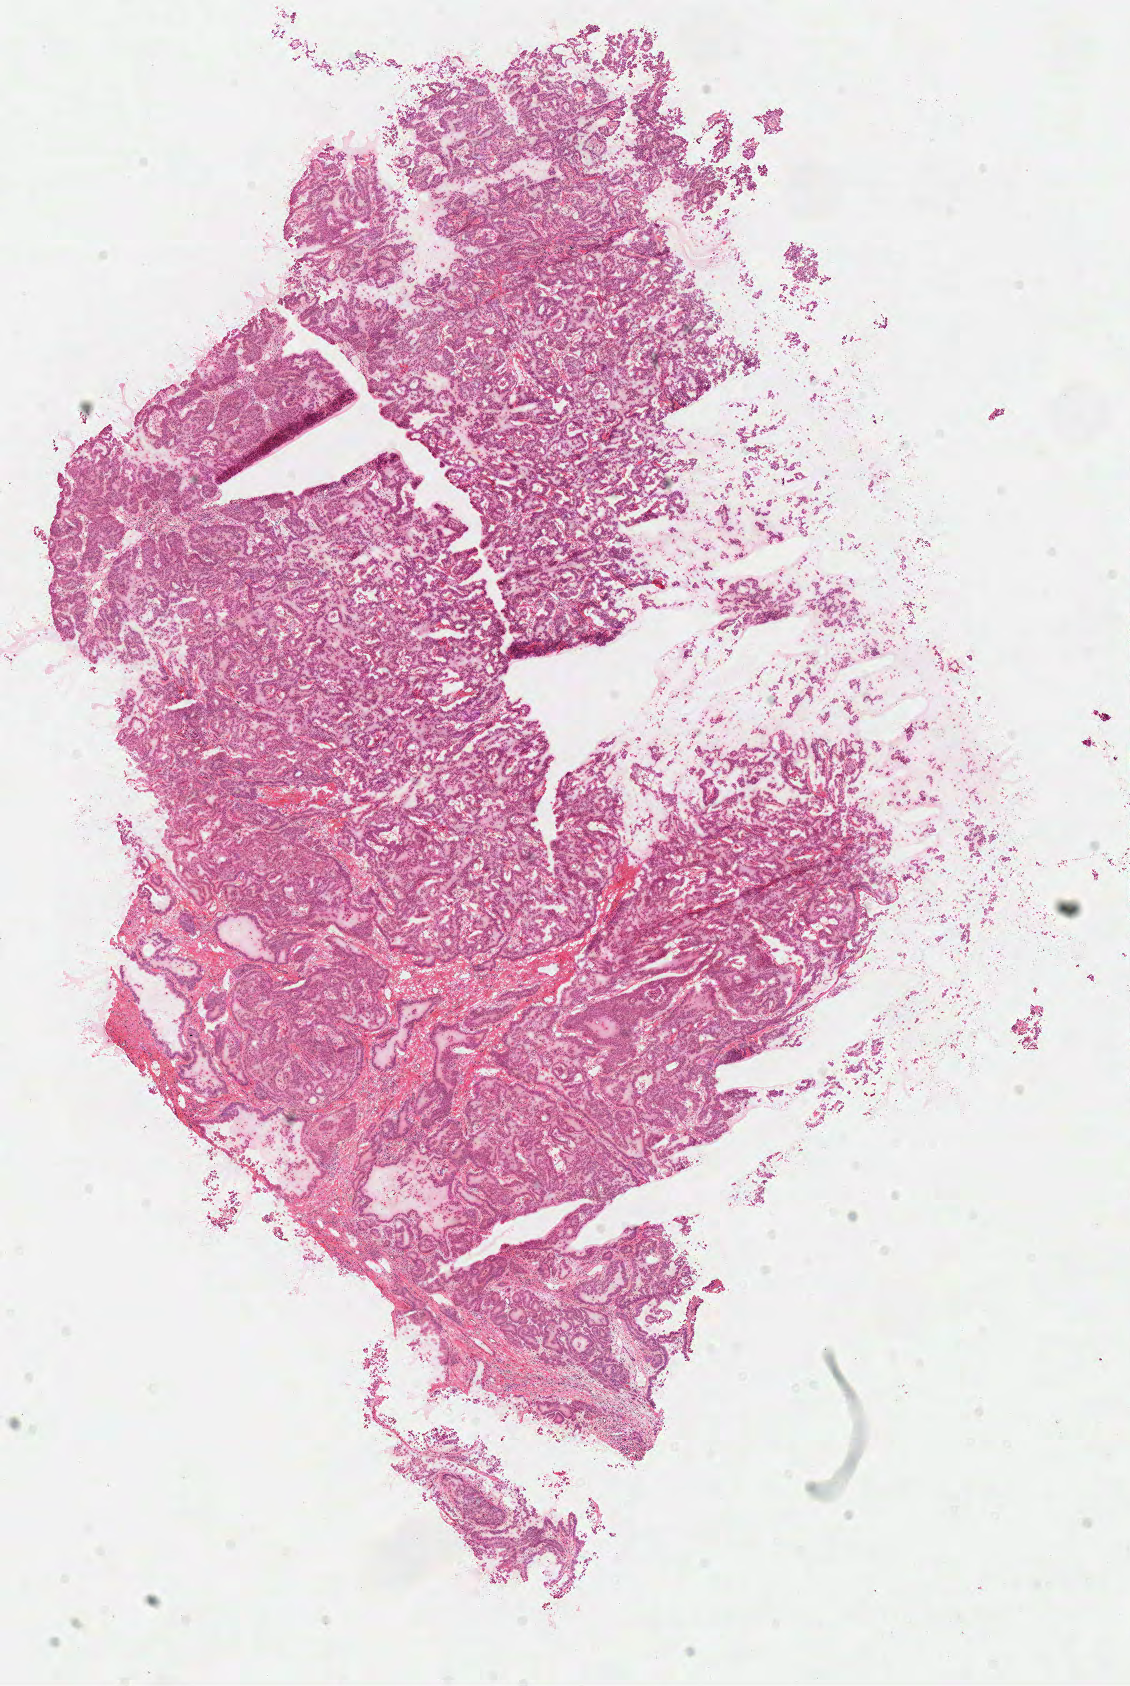
Hematoxylin and eosin (H&E) stained whole-slide image, shown as a low-resolution overview of the whole scanned area (about 8.9 x 13.3 mm, acquisition: 40x scan), frozen section, primary tumour sample from the kidney. Male, age 61 years at initial diagnosis. Pathologist review of this section (percent, as recorded): tumour cells 90%, tumour nuclei 80%, normal cells 0%, stromal cells 10%, necrosis 0%.
- pathologic diagnosis: Papillary adenocarcinoma, NOS
- AJCC pathologic stage: IV
- laterality: left
- TNM: T3a N1 M1
- lymph nodes positive (case pathology): 30 of 30 examined